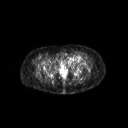
FDG PET of an extremity soft-tissue mass (from a PET/CT study), one axial slice. Position 47 of 267 along the scan axis. 3.27 mm slice thickness. 128 × 128 image matrix, field of view 700 × 700 mm. Patient: female, 47 years. Case-level facts recorded for this patient, not image findings: histological type: myxofibrosarcoma; grade: intermediate; site of the primary tumour: left thigh.
Outlined on this slice (expert contour drawn on MRI and transferred to this co-registered scan by the dataset authors):
- gross tumour volume including surrounding oedema: bounding box [x1, y1, x2, y2] px = [65, 55, 84, 63]